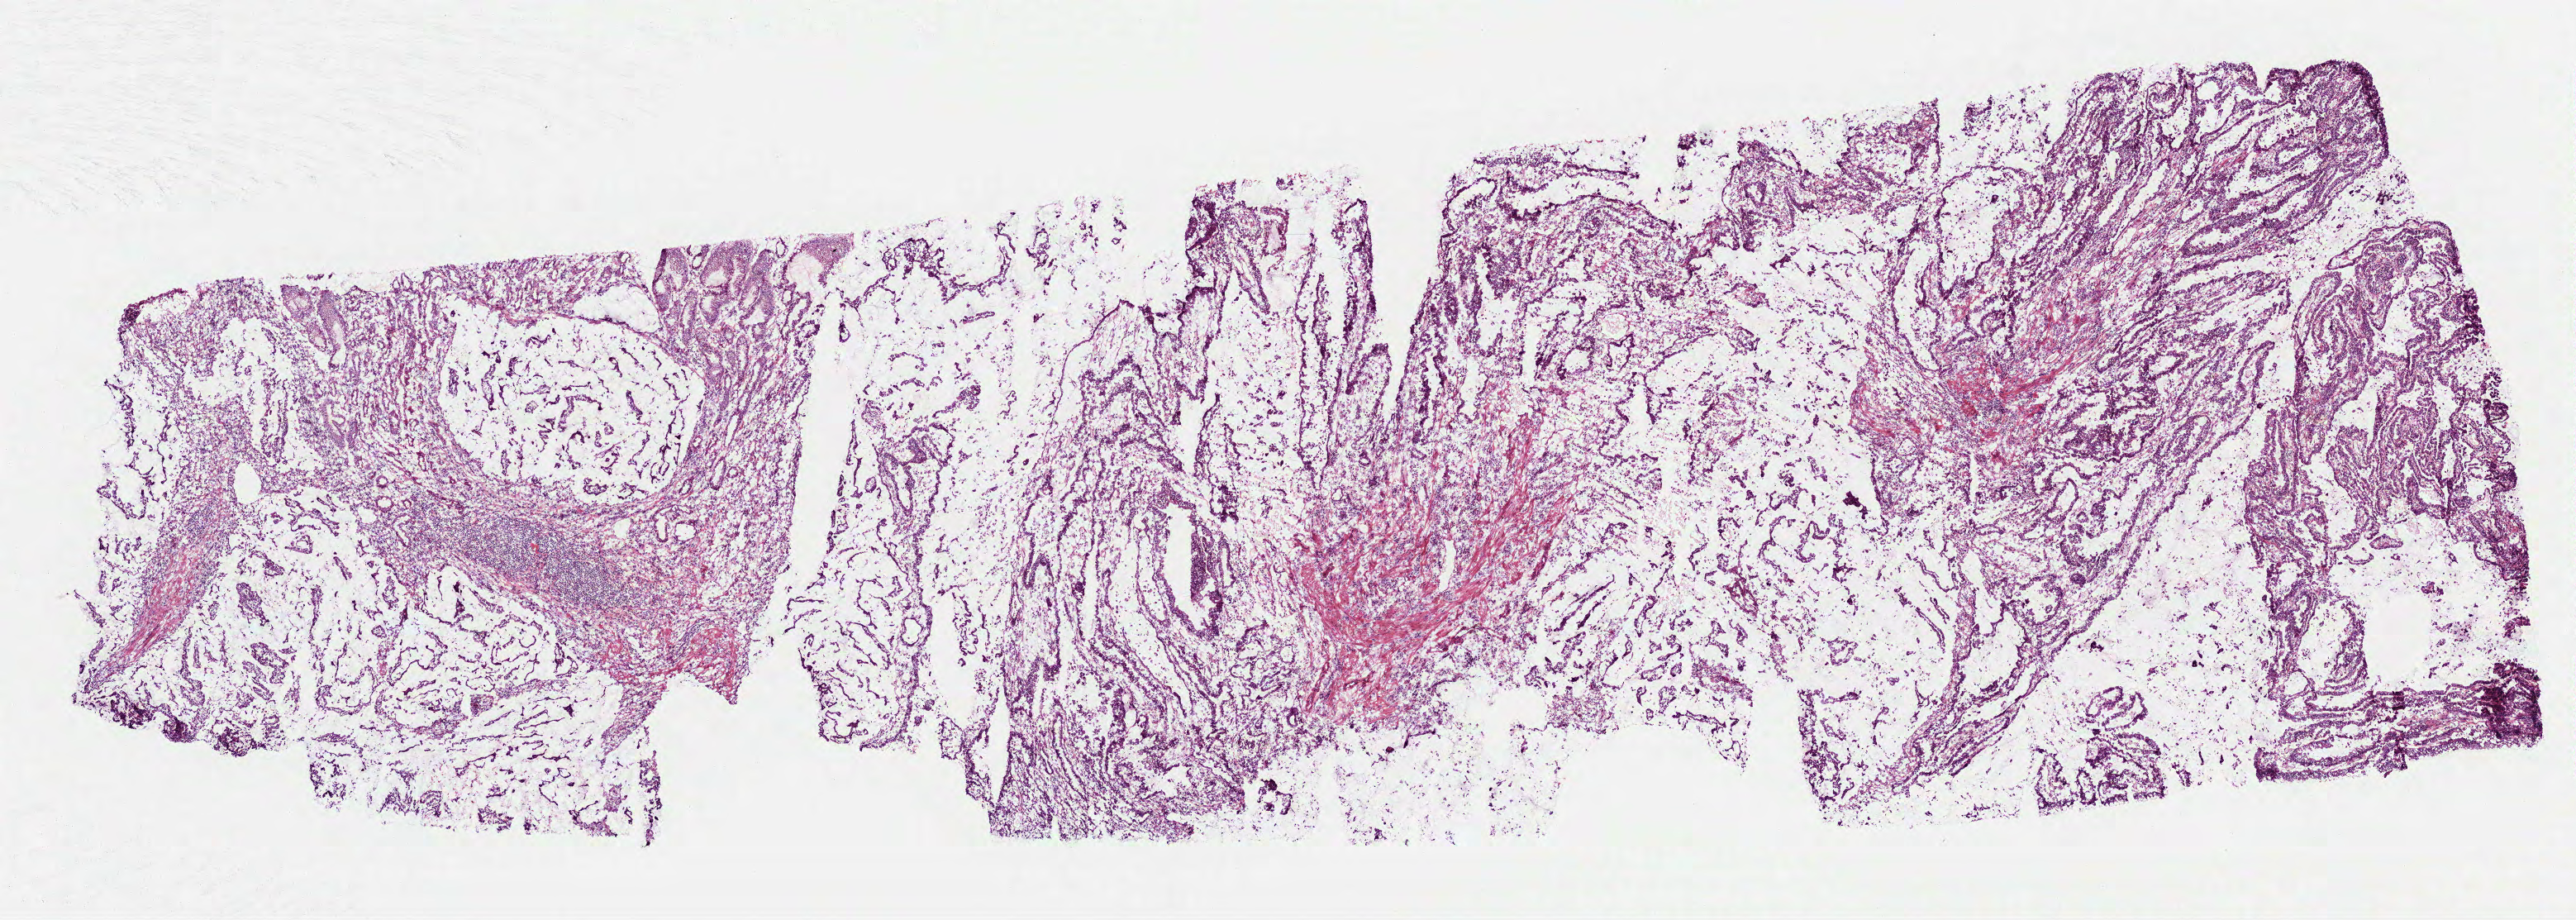
Whole-slide histology image, H&E-stained — shown as a low-resolution overview of the whole scanned area (about 12.6 x 4.5 mm, from a 40x scan). Frozen section. Stomach, primary tumour sample. Female patient. Histologic grade: G2 (moderately differentiated). Slide review estimates, as recorded: tumour cells 100%, tumour nuclei 60%, normal cells 0%, stromal cells 0%, necrosis 0%. Infiltration values recorded for this section: lymphocyte infiltration 20%, monocyte infiltration 0%, neutrophil infiltration 15%.
Pathologic diagnosis: Mucinous adenocarcinoma. Lymph nodes positive (case pathology): 16 of 53 examined. AJCC pathologic stage: IV (6th edition).